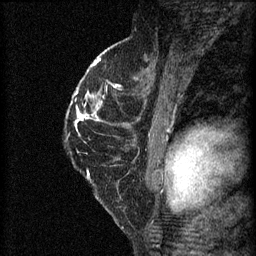
Breast MRI (dynamic contrast-enhanced), one sagittal slice; position 38 of 60 along the scan axis; 3 images stored at this slice position (order not interpretable as contrast timing); 1.5 T; TE 4.2 ms, TR 8.2 ms; 256 × 256 image matrix, field of view 180 × 180 mm. Female patient, age 45 years.
Outlined on this slice (semi-automatically segmented with operator editing):
- analysis volume of interest (the breast-tissue region the enhancement analysis was run in; not a lesion): bounding box [x1, y1, x2, y2] px = [67, 98, 104, 137]
- tumour enhancement mask (voxels above the 70 % enhancement threshold inside the analysis volume of interest): [76, 118, 99, 127]